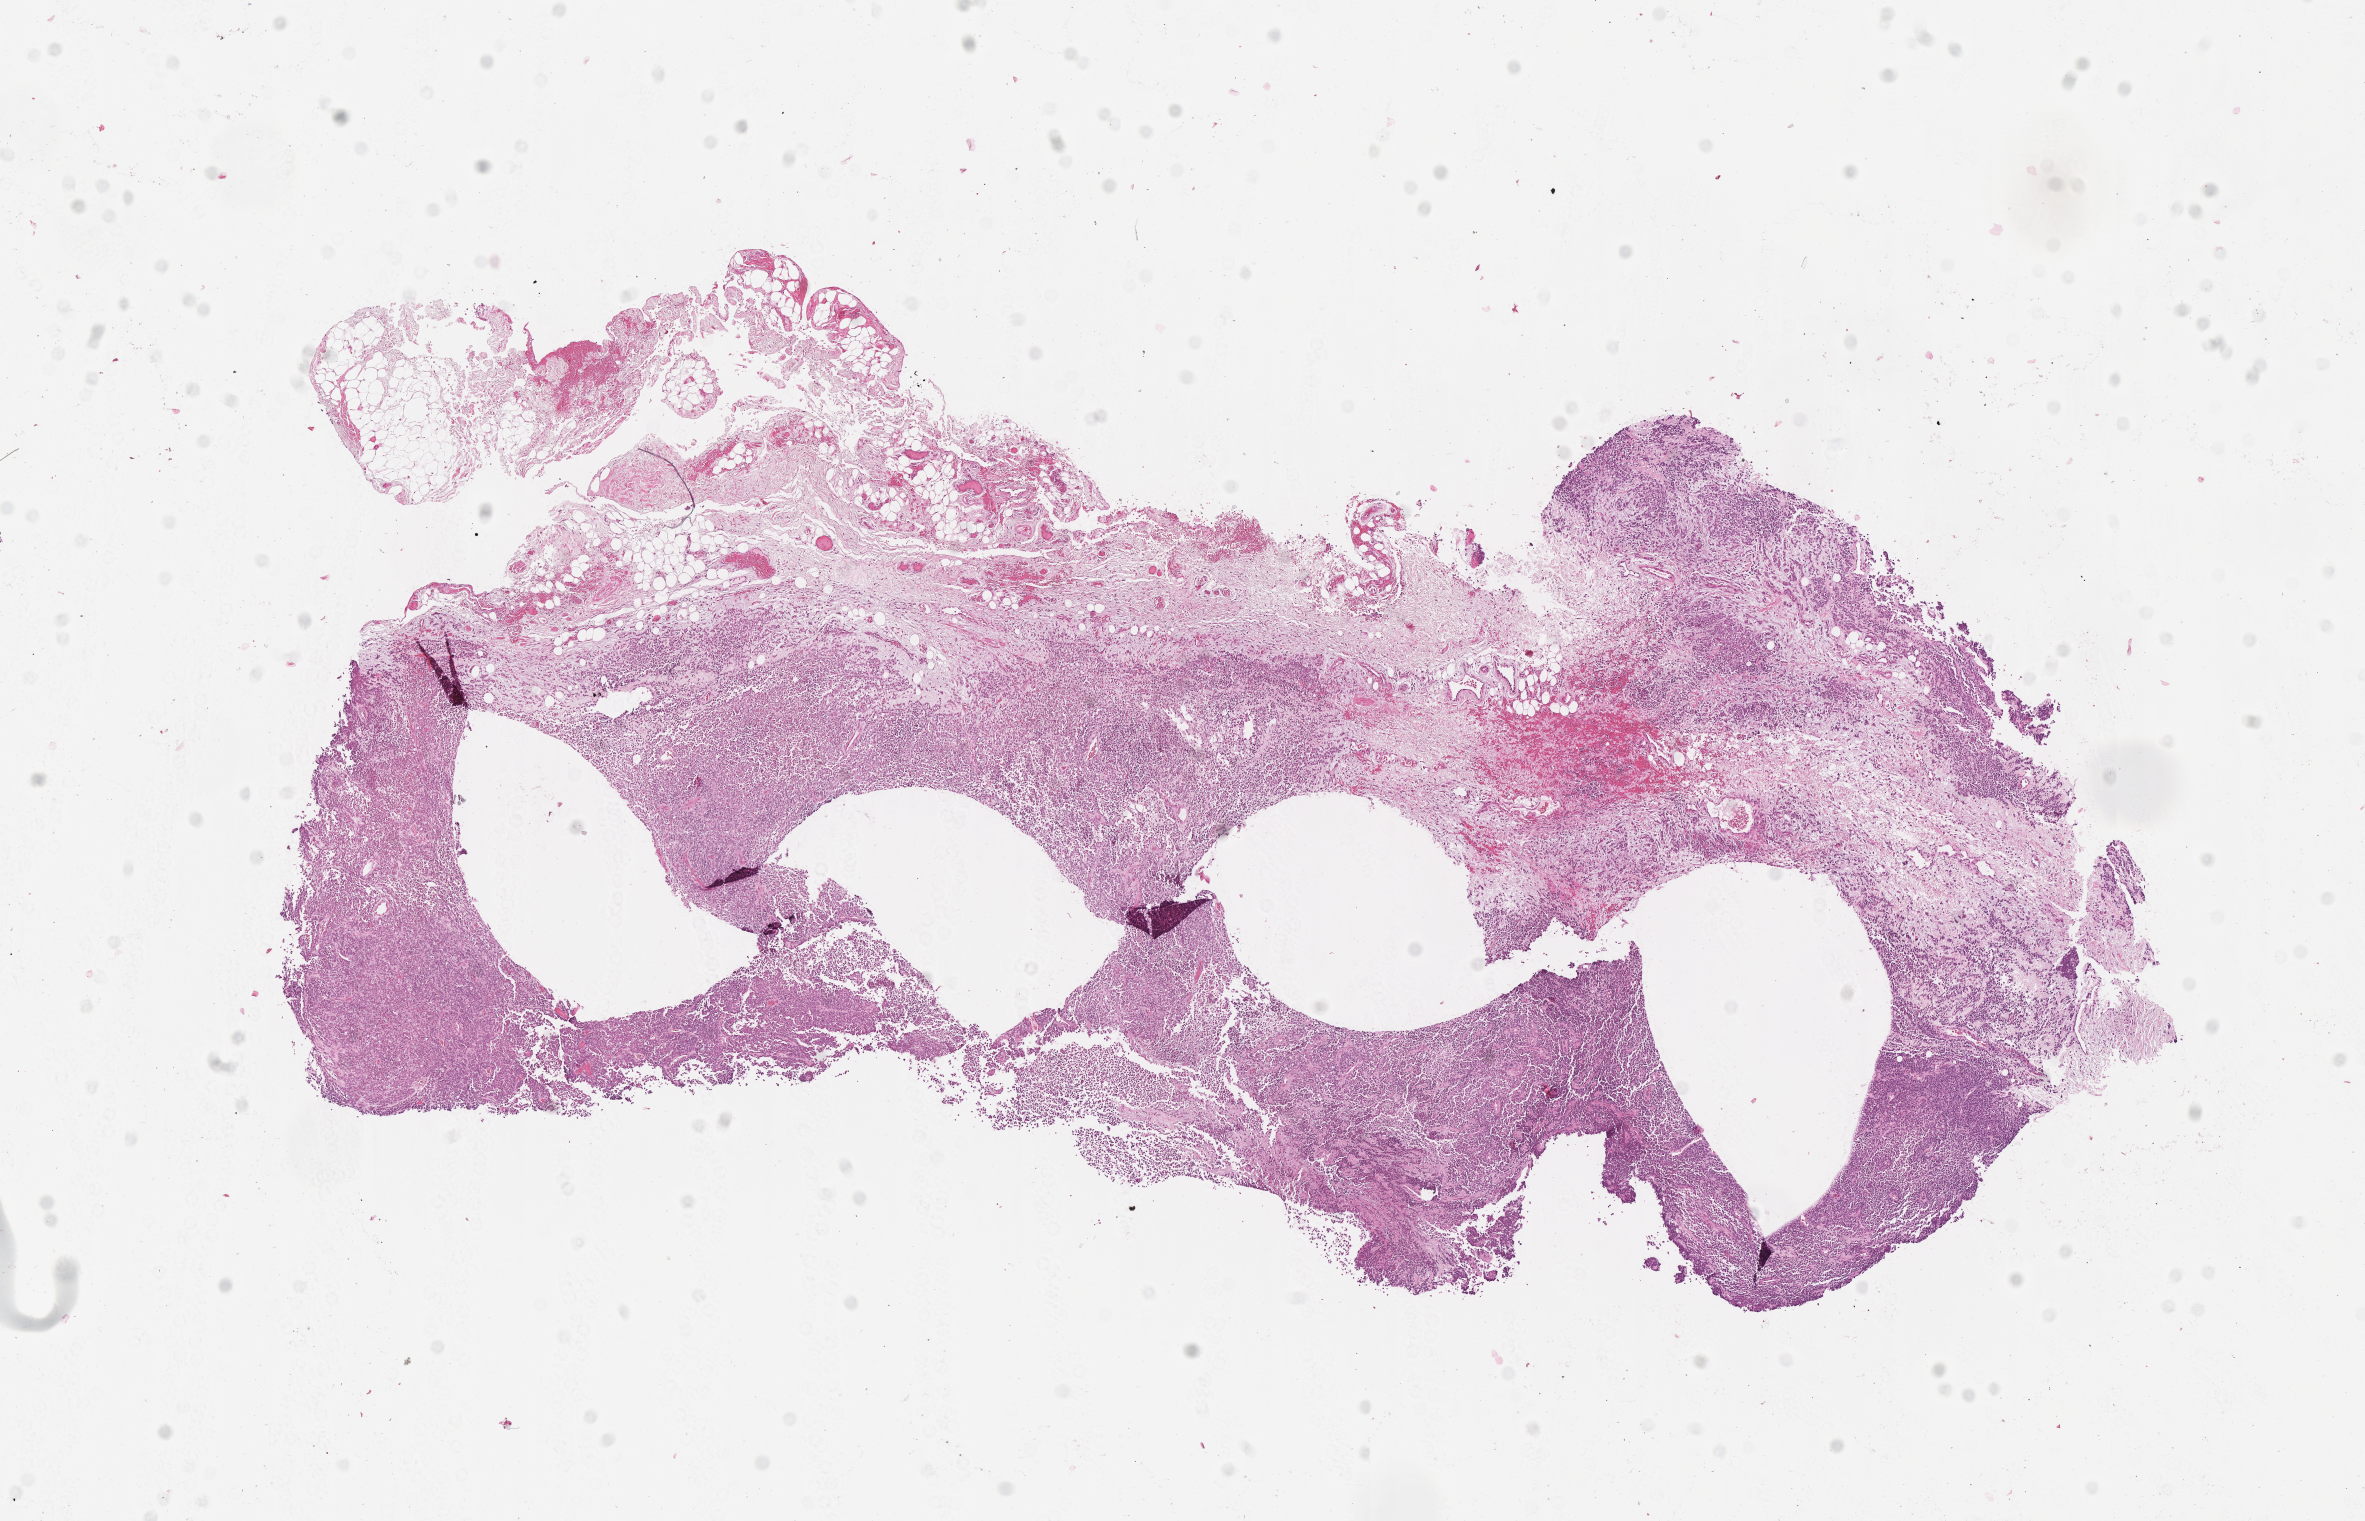
Digitized H&E-stained section of tumor tissue, shown as a low-resolution overview of the whole scanned area (about 9.6 x 6.1 mm), formalin-fixed, paraffin-embedded (FFPE) tissue, site: orbit, right. Patient: female, age 12.4 years at diagnosis.
Metastatic status at presentation (as recorded): non-metastatic. Diagnosis: rhabdomyosarcoma; histological classification: alveolar rhabdomyosarcoma. Stage (as recorded): 1.